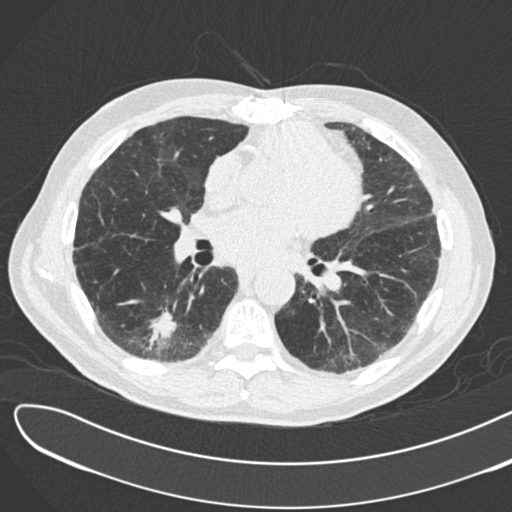
Low-dose screening chest CT, one axial slice. Slice 84 of 183 in the series (ordered by position). Reconstruction kernel B30f. Lung window (W 1500 / L -600 HU). 512 × 512 image matrix, field of view 370 × 370 mm.
Outlined on this slice (expert manual segmentation):
- lesion 1 (tumor, lower lobe of right lung): bounding box <145,311,177,351> (left, top, right, bottom; pixels)